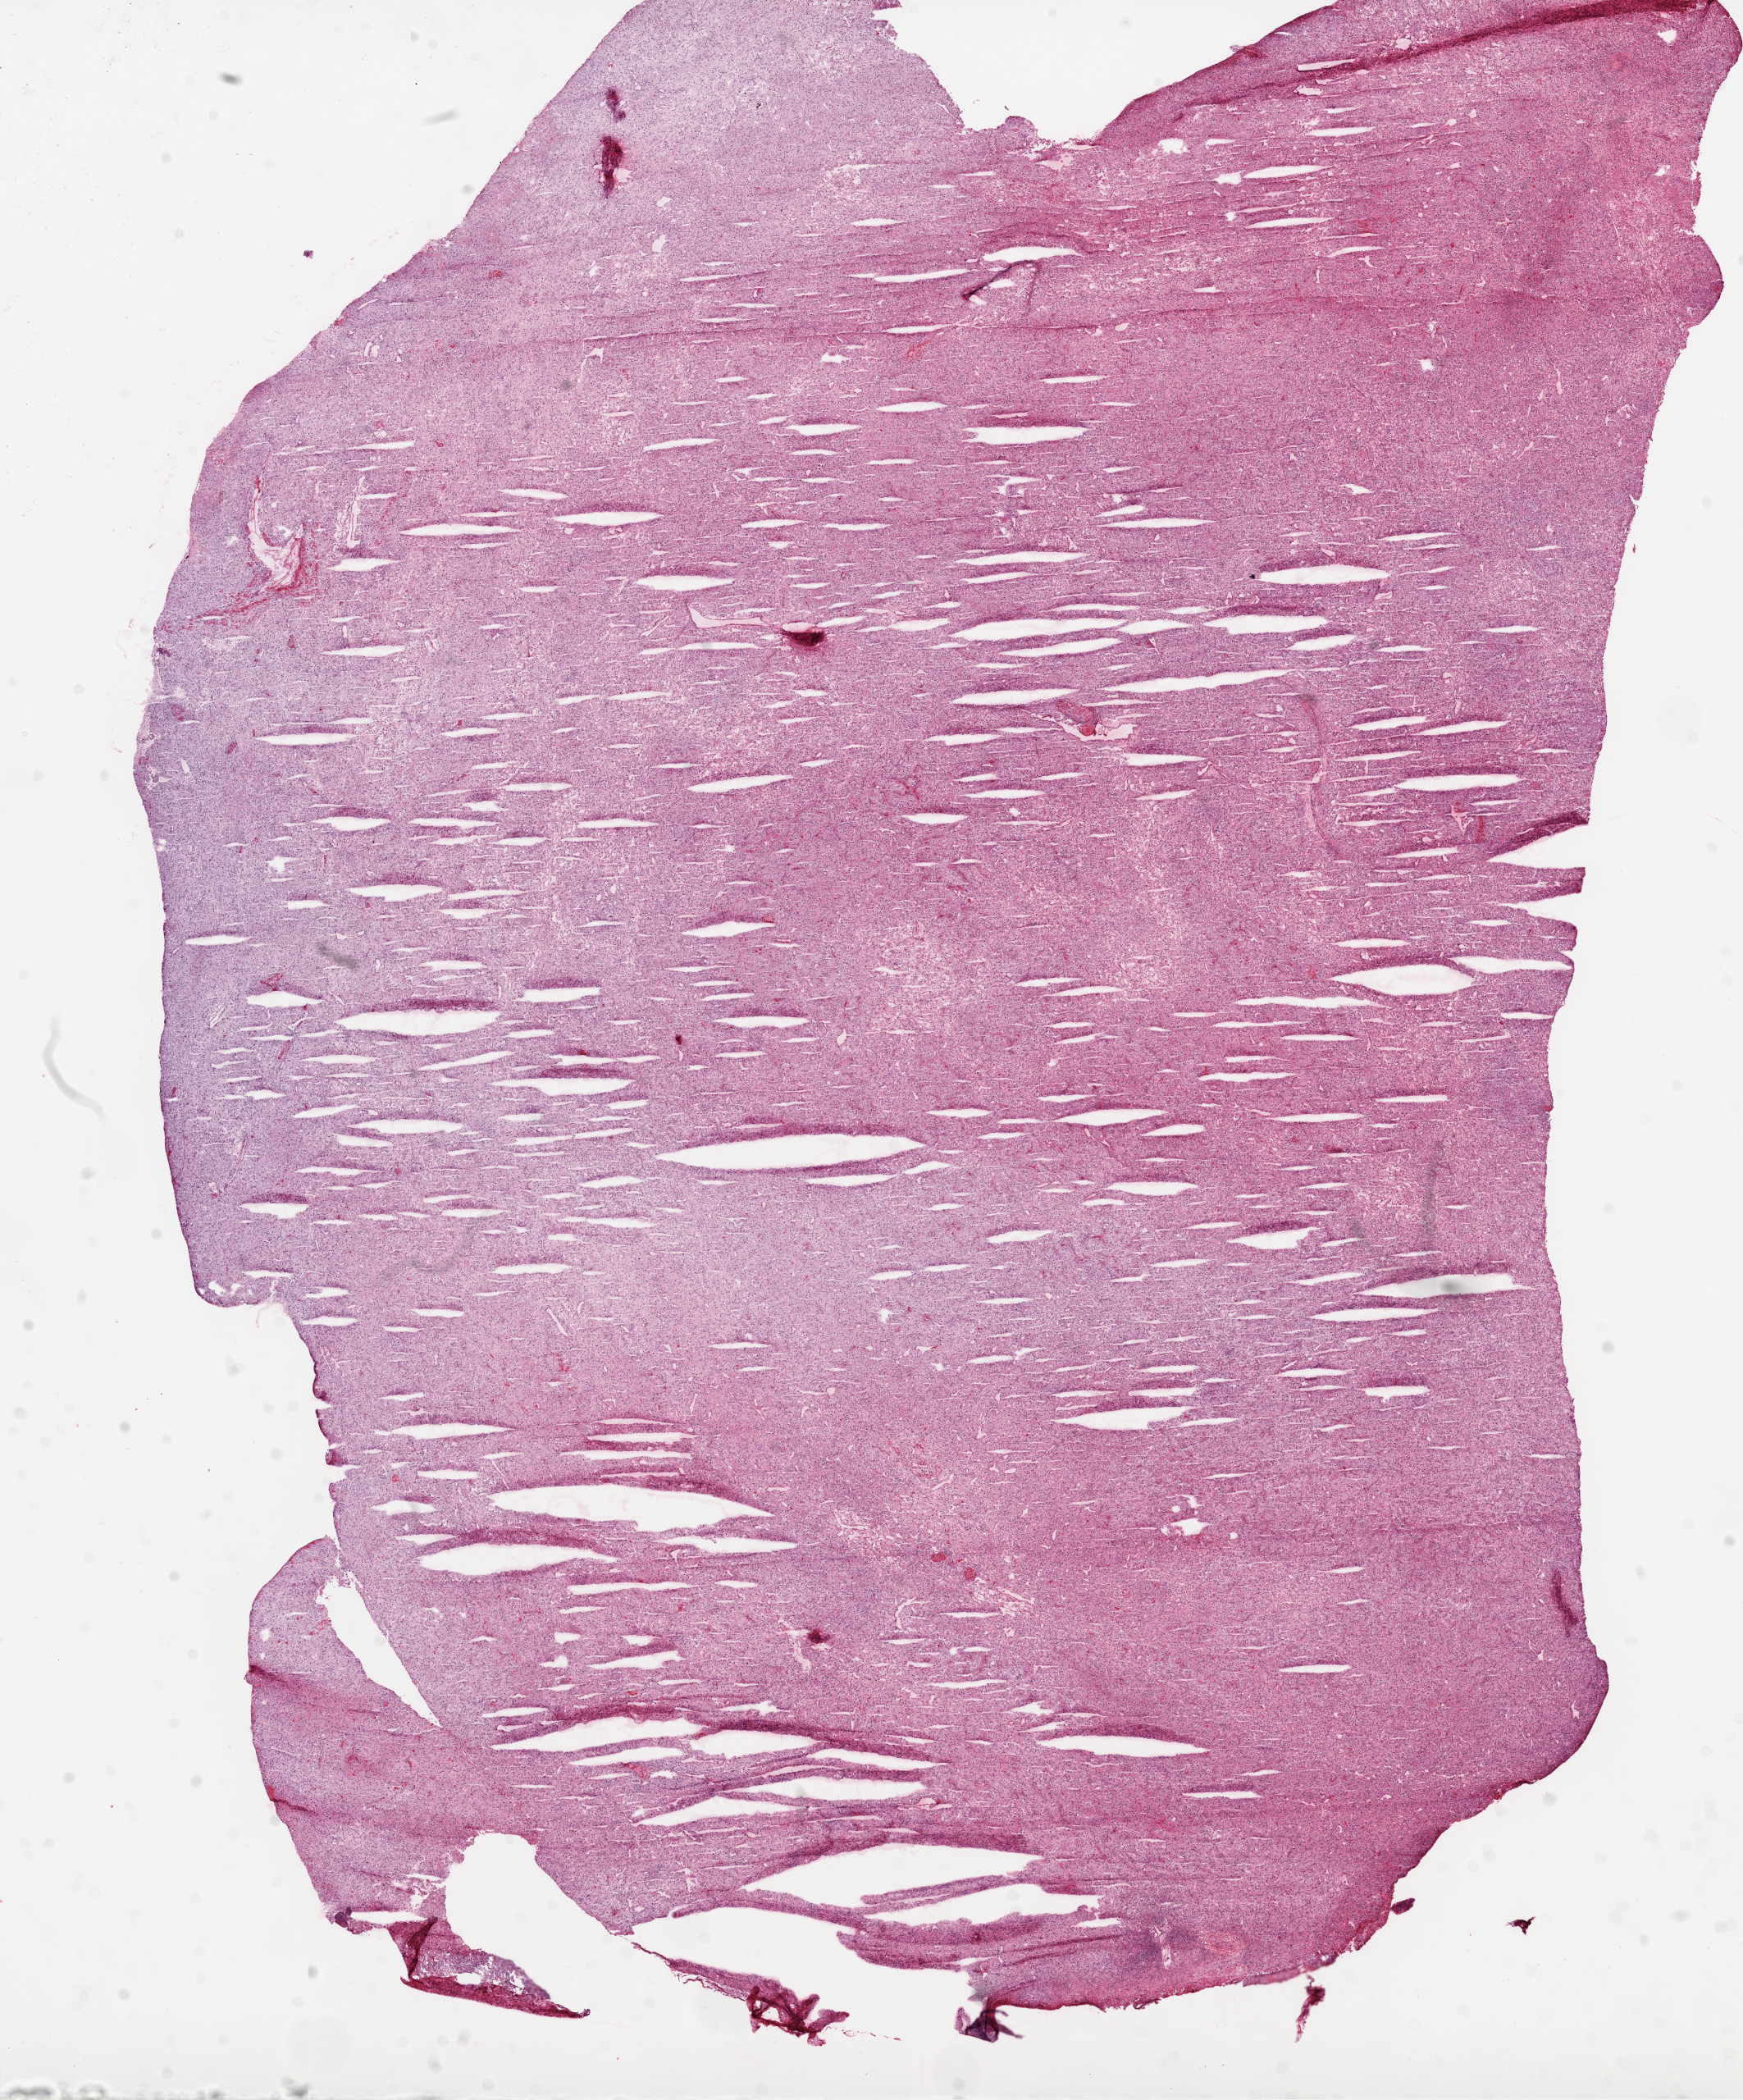
Digitized Hematoxylin and eosin (H&E) stained tissue section (whole slide) — a low-resolution overview of the entire scanned area, about 17.1 x 20.5 mm (slide scanned at 20x); frozen section; sample: primary tumour, kidney. Male patient; age at initial diagnosis 84 years. Histologic grade: G4 (undifferentiated). Composition of this section per pathologist review: tumour cells 95%, tumour nuclei 90%, normal cells 0%, stromal cells 5%, necrosis 0%. Inflammatory infiltration, as recorded: lymphocyte infiltration 2%, monocyte infiltration 0%, neutrophil infiltration 0%.
Diagnosis: Clear cell adenocarcinoma, NOS. AJCC pathologic stage: IV. Laterality: left.